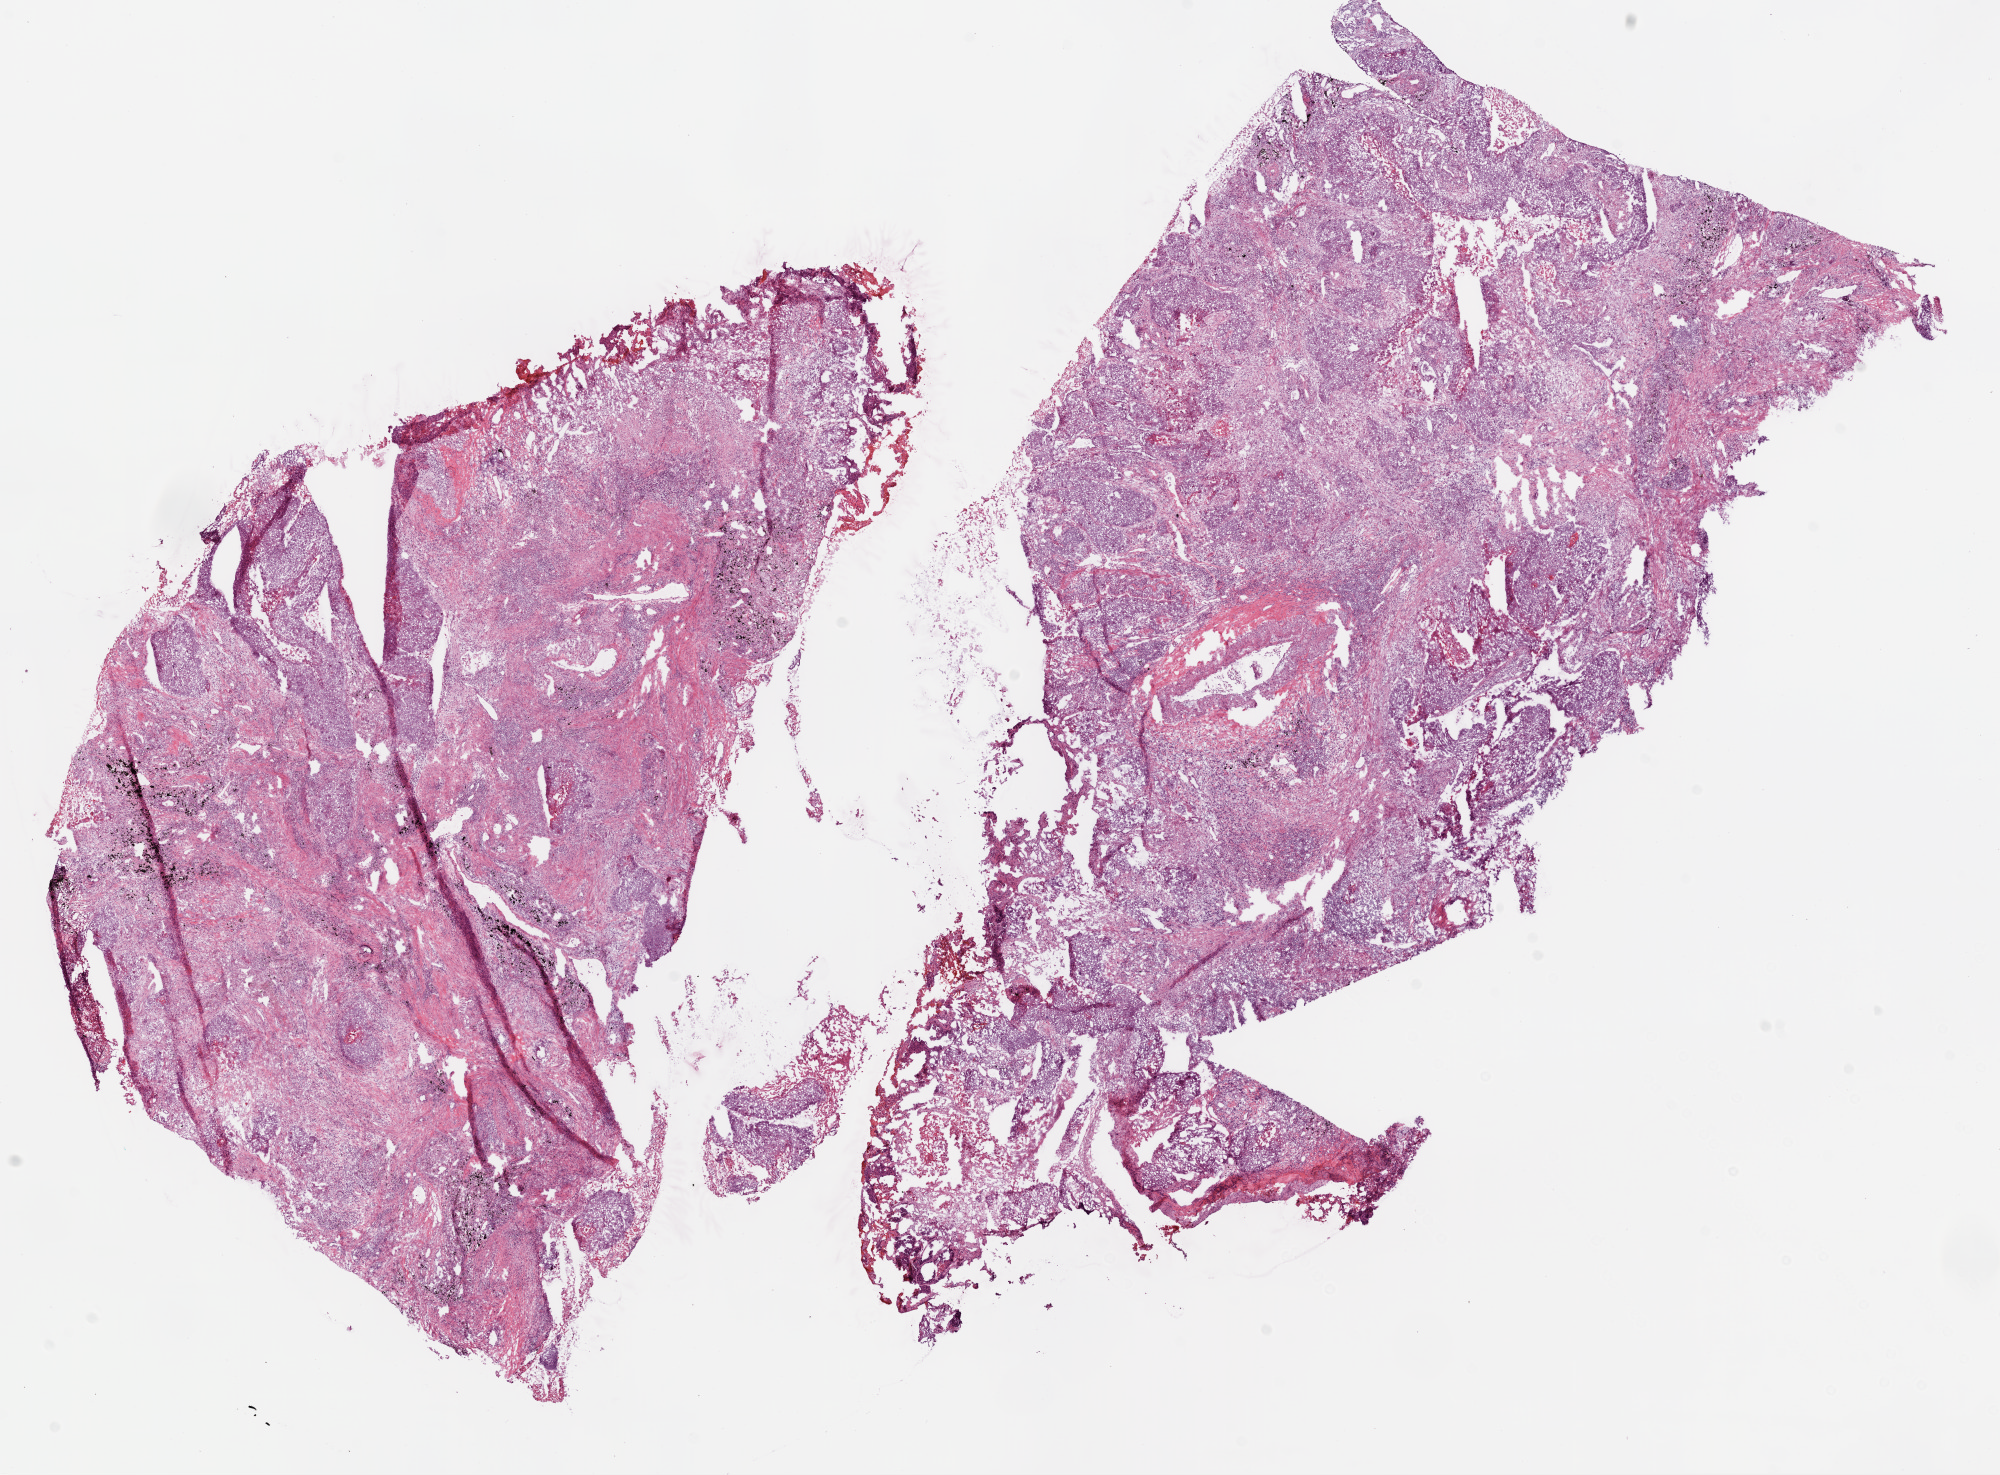
Whole-slide histology image, Hematoxylin and eosin (H&E) stained — shown as a low-resolution overview of the whole scanned area (about 16.0 x 11.8 mm, acquisition: 20x scan), frozen section from the top of the tissue portion, primary tumour sample from the lung. Male, age 70 years at initial diagnosis. Composition of this section per pathologist review: tumour cells 74%, tumour nuclei 60%, normal cells 0%, stromal cells 17%, necrosis 9%. Inflammatory infiltration, as recorded: lymphocyte infiltration 20%, monocyte infiltration 2%, neutrophil infiltration 10%.
* AJCC pathologic stage: IB
* pathologic diagnosis: Squamous cell carcinoma, NOS (upper lobe, lung)